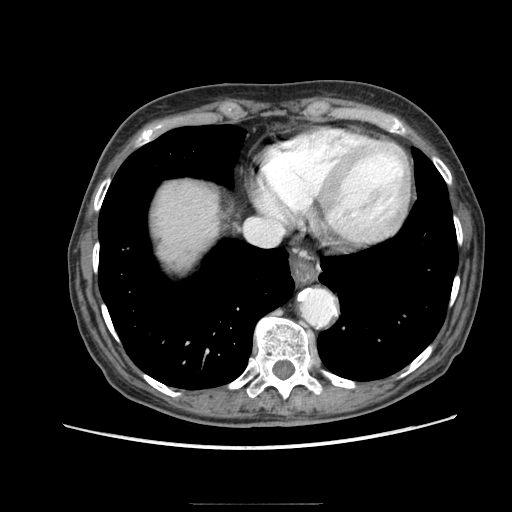
Contrast-enhanced abdominal CT (liver protocol), one axial slice; slice 76 of 83 in the series (ordered by position); reconstruction kernel STANDARD; 140 kVp; soft-tissue window (W 400 / L 40 HU); 2.5 mm slice thickness; 512 × 512 image matrix, field of view 360 × 360 mm. Case-level facts recorded for this patient, not image findings: diagnosis: hepatocellular carcinoma (patient treated with transarterial chemoembolisation; whether this scan precedes or follows treatment is not stated here); TNM stage (as recorded): Stage-I; Child-Pugh class: A; tumour differentiation: moderately differentiated; tumour nodularity: uninodular.
Outlined on this slice (semi-automatic segmentation, software-assisted and operator-edited):
- liver parenchyma outside the tumour (the mass and vessels are separate outlines, so this box may not span the whole liver): bounding box [x1, y1, x2, y2] px = [154, 182, 218, 268]